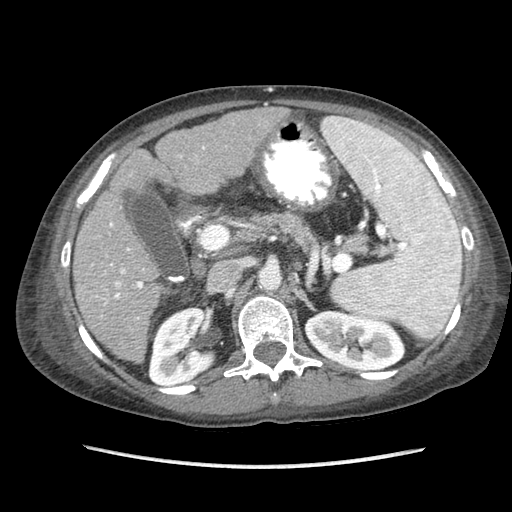
Contrast-enhanced abdominal CT (liver protocol), one axial slice; position 41 of 87 along the scan axis; reconstruction kernel STANDARD; 120 kVp; soft-tissue window (W 400 / L 40 HU); 2.5 mm slice thickness; 512 × 512 image matrix, field of view 340 × 340 mm. Case-level facts recorded for this patient, not image findings: diagnosis: hepatocellular carcinoma (patient treated with transarterial chemoembolisation; whether this scan precedes or follows treatment is not stated here); TNM stage (as recorded): Stage-IIIB.
Outlined on this slice (semi-automatically segmented with operator editing):
- liver parenchyma outside the tumour (the mass and vessels are separate outlines, so this box may not span the whole liver): bounding box <74,108,288,362> (left, top, right, bottom; pixels)
- liver vessels: <92,147,205,305>